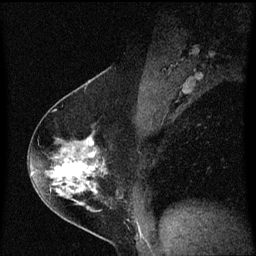
Breast MRI (dynamic contrast-enhanced), one sagittal slice. Slice 36 of 60 in the series (ordered by position). Dynamic contrast-enhanced series, image 2 of 3 at this slice position (ordered by acquisition). 1.5 T. TE 4.2 ms, TR 8.4 ms. 256 × 256 image matrix, field of view 200 × 200 mm. Patient: female, 54 years. Case-level facts recorded for this patient, not image findings: setting: breast cancer imaged before/during neoadjuvant chemotherapy; receptor status: HER2-positive.
Outlined on this slice (semi-automatically segmented with operator editing):
- analysis volume of interest (the breast-tissue region the enhancement analysis was run in; not a lesion): bounding box (x1, y1, x2, y2) in pixels: (32, 128, 119, 213)
- tumour enhancement mask (voxels above the 70 % enhancement threshold inside the analysis volume of interest): (54, 138, 97, 193)